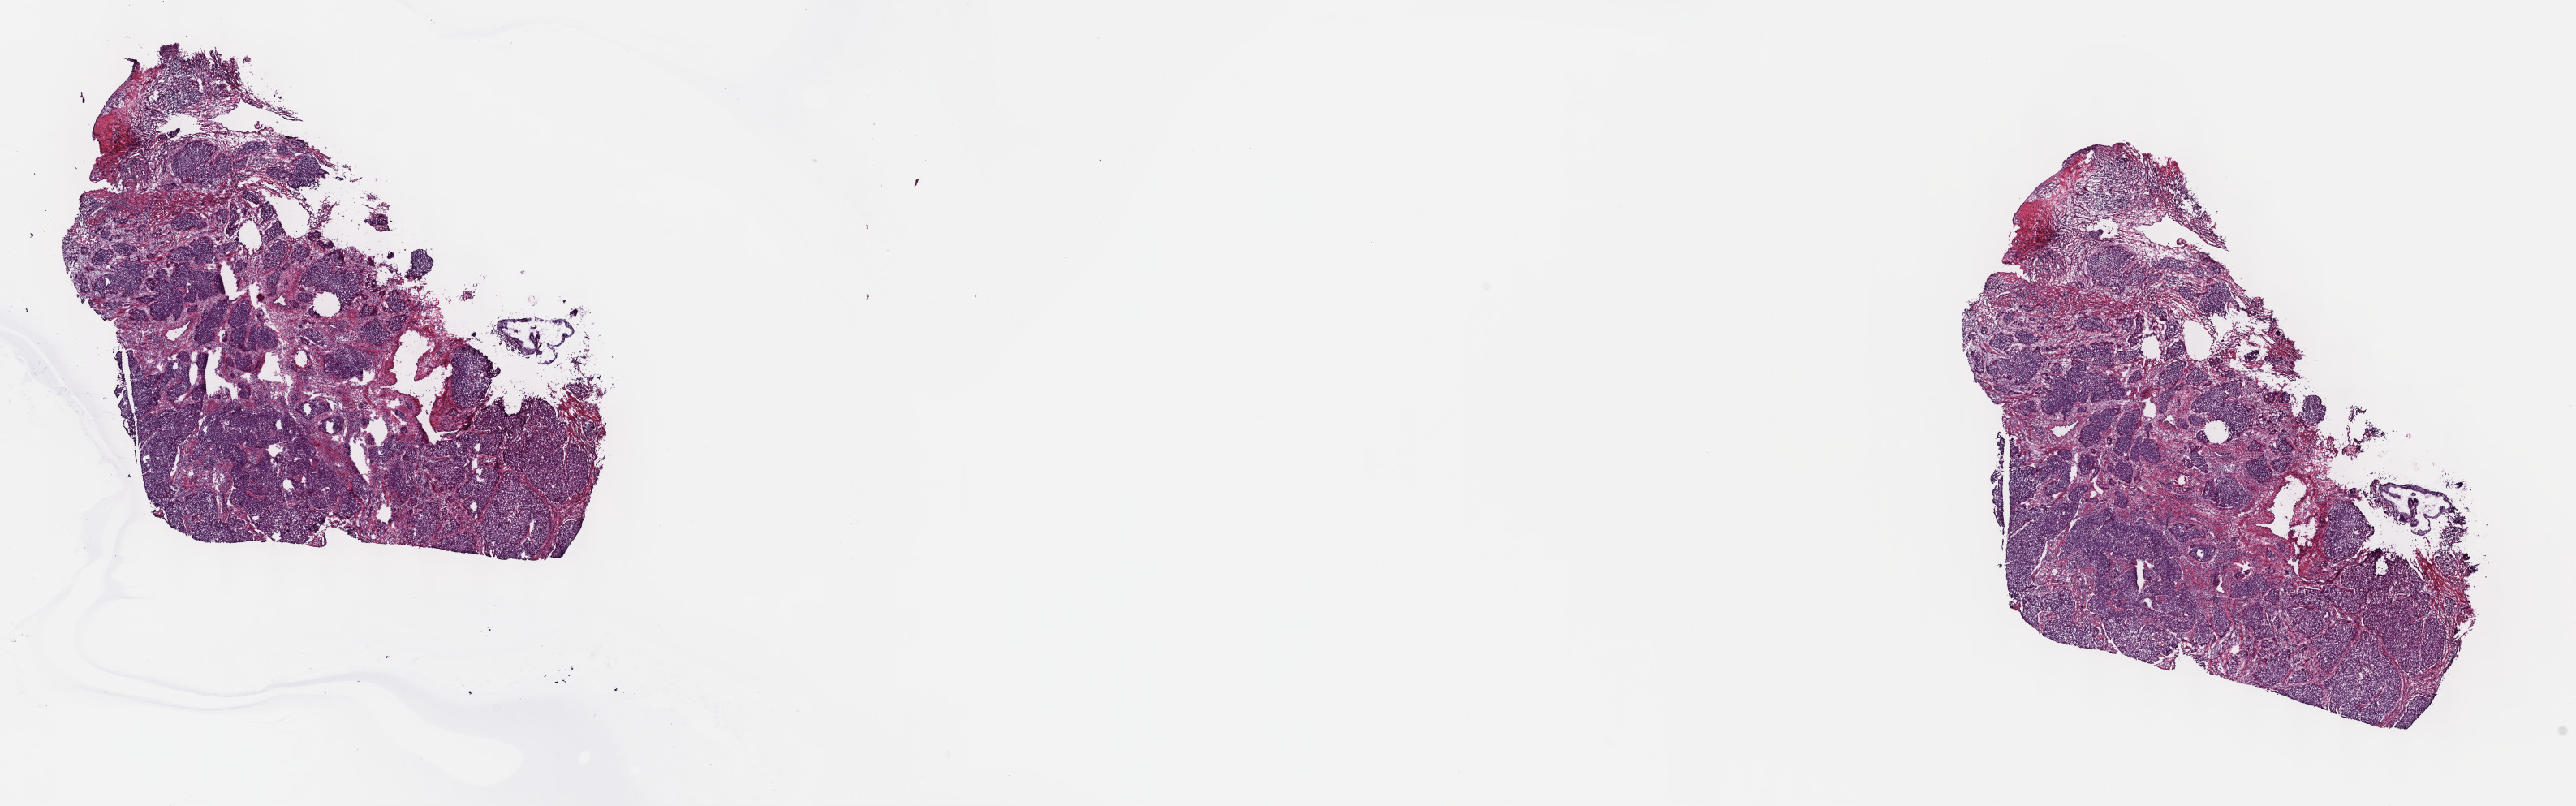
Digitized H&E-stained tissue section (whole slide) — shown as a low-resolution overview of the whole scanned area (about 25.7 x 8.0 mm); frozen section from the top of the tissue portion; primary tumour sample from the cervix. Female patient; age at initial diagnosis 42 years. Histologic grade: G2 (moderately differentiated). Slide review estimates, as recorded: tumour cells 100%, tumour nuclei 65%, normal cells 0%, stromal cells 0%, necrosis 0%. Inflammatory infiltration, as recorded: lymphocyte infiltration 5%, monocyte infiltration 0%, neutrophil infiltration 0%.
- diagnosis: Squamous cell carcinoma, keratinizing, NOS (cervix uteri)
- FIGO stage: IIA